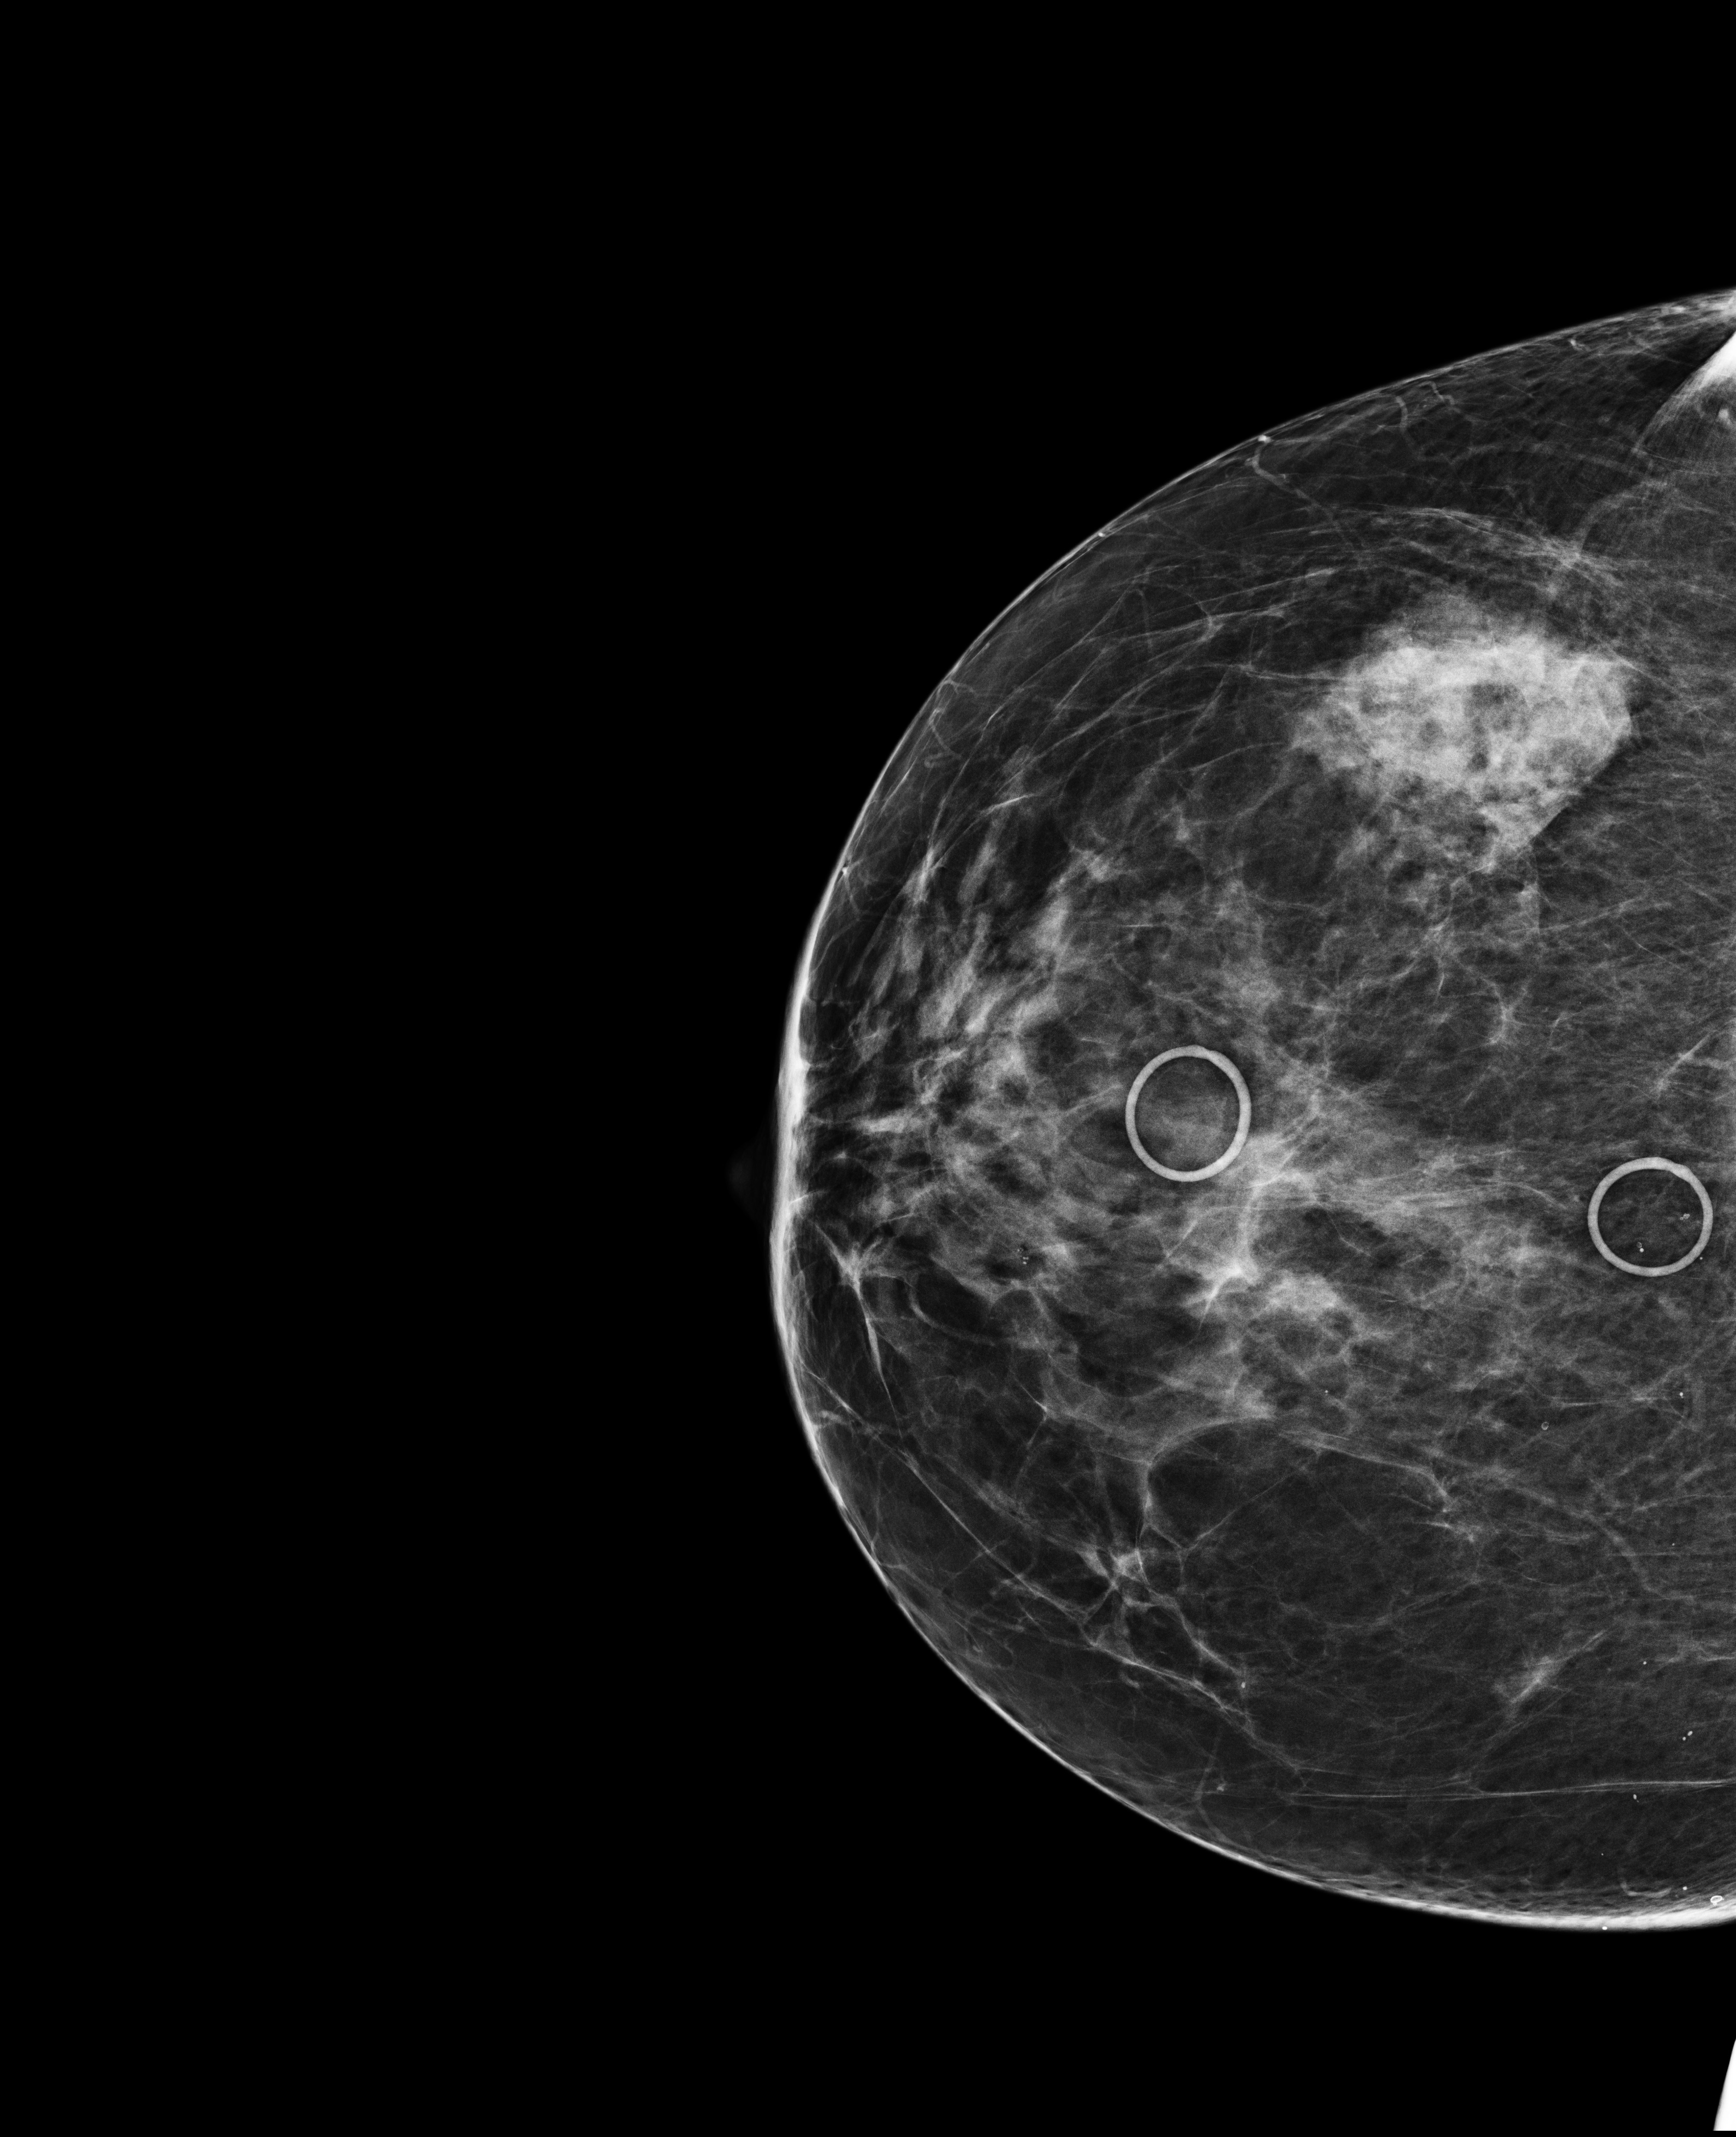
Digital mammogram (FFDM); right breast; CC view; annual screening mammography examination; system: Selenia Dimensions. Patient aged 60 years (female).
- breast density at the screening exam (both breasts): heterogeneously dense (BI-RADS density category c)
- final BI-RADS assessment for this screening round (tomosynthesis exam, both breasts): category 1
- recall: recalled for additional imaging after this screen